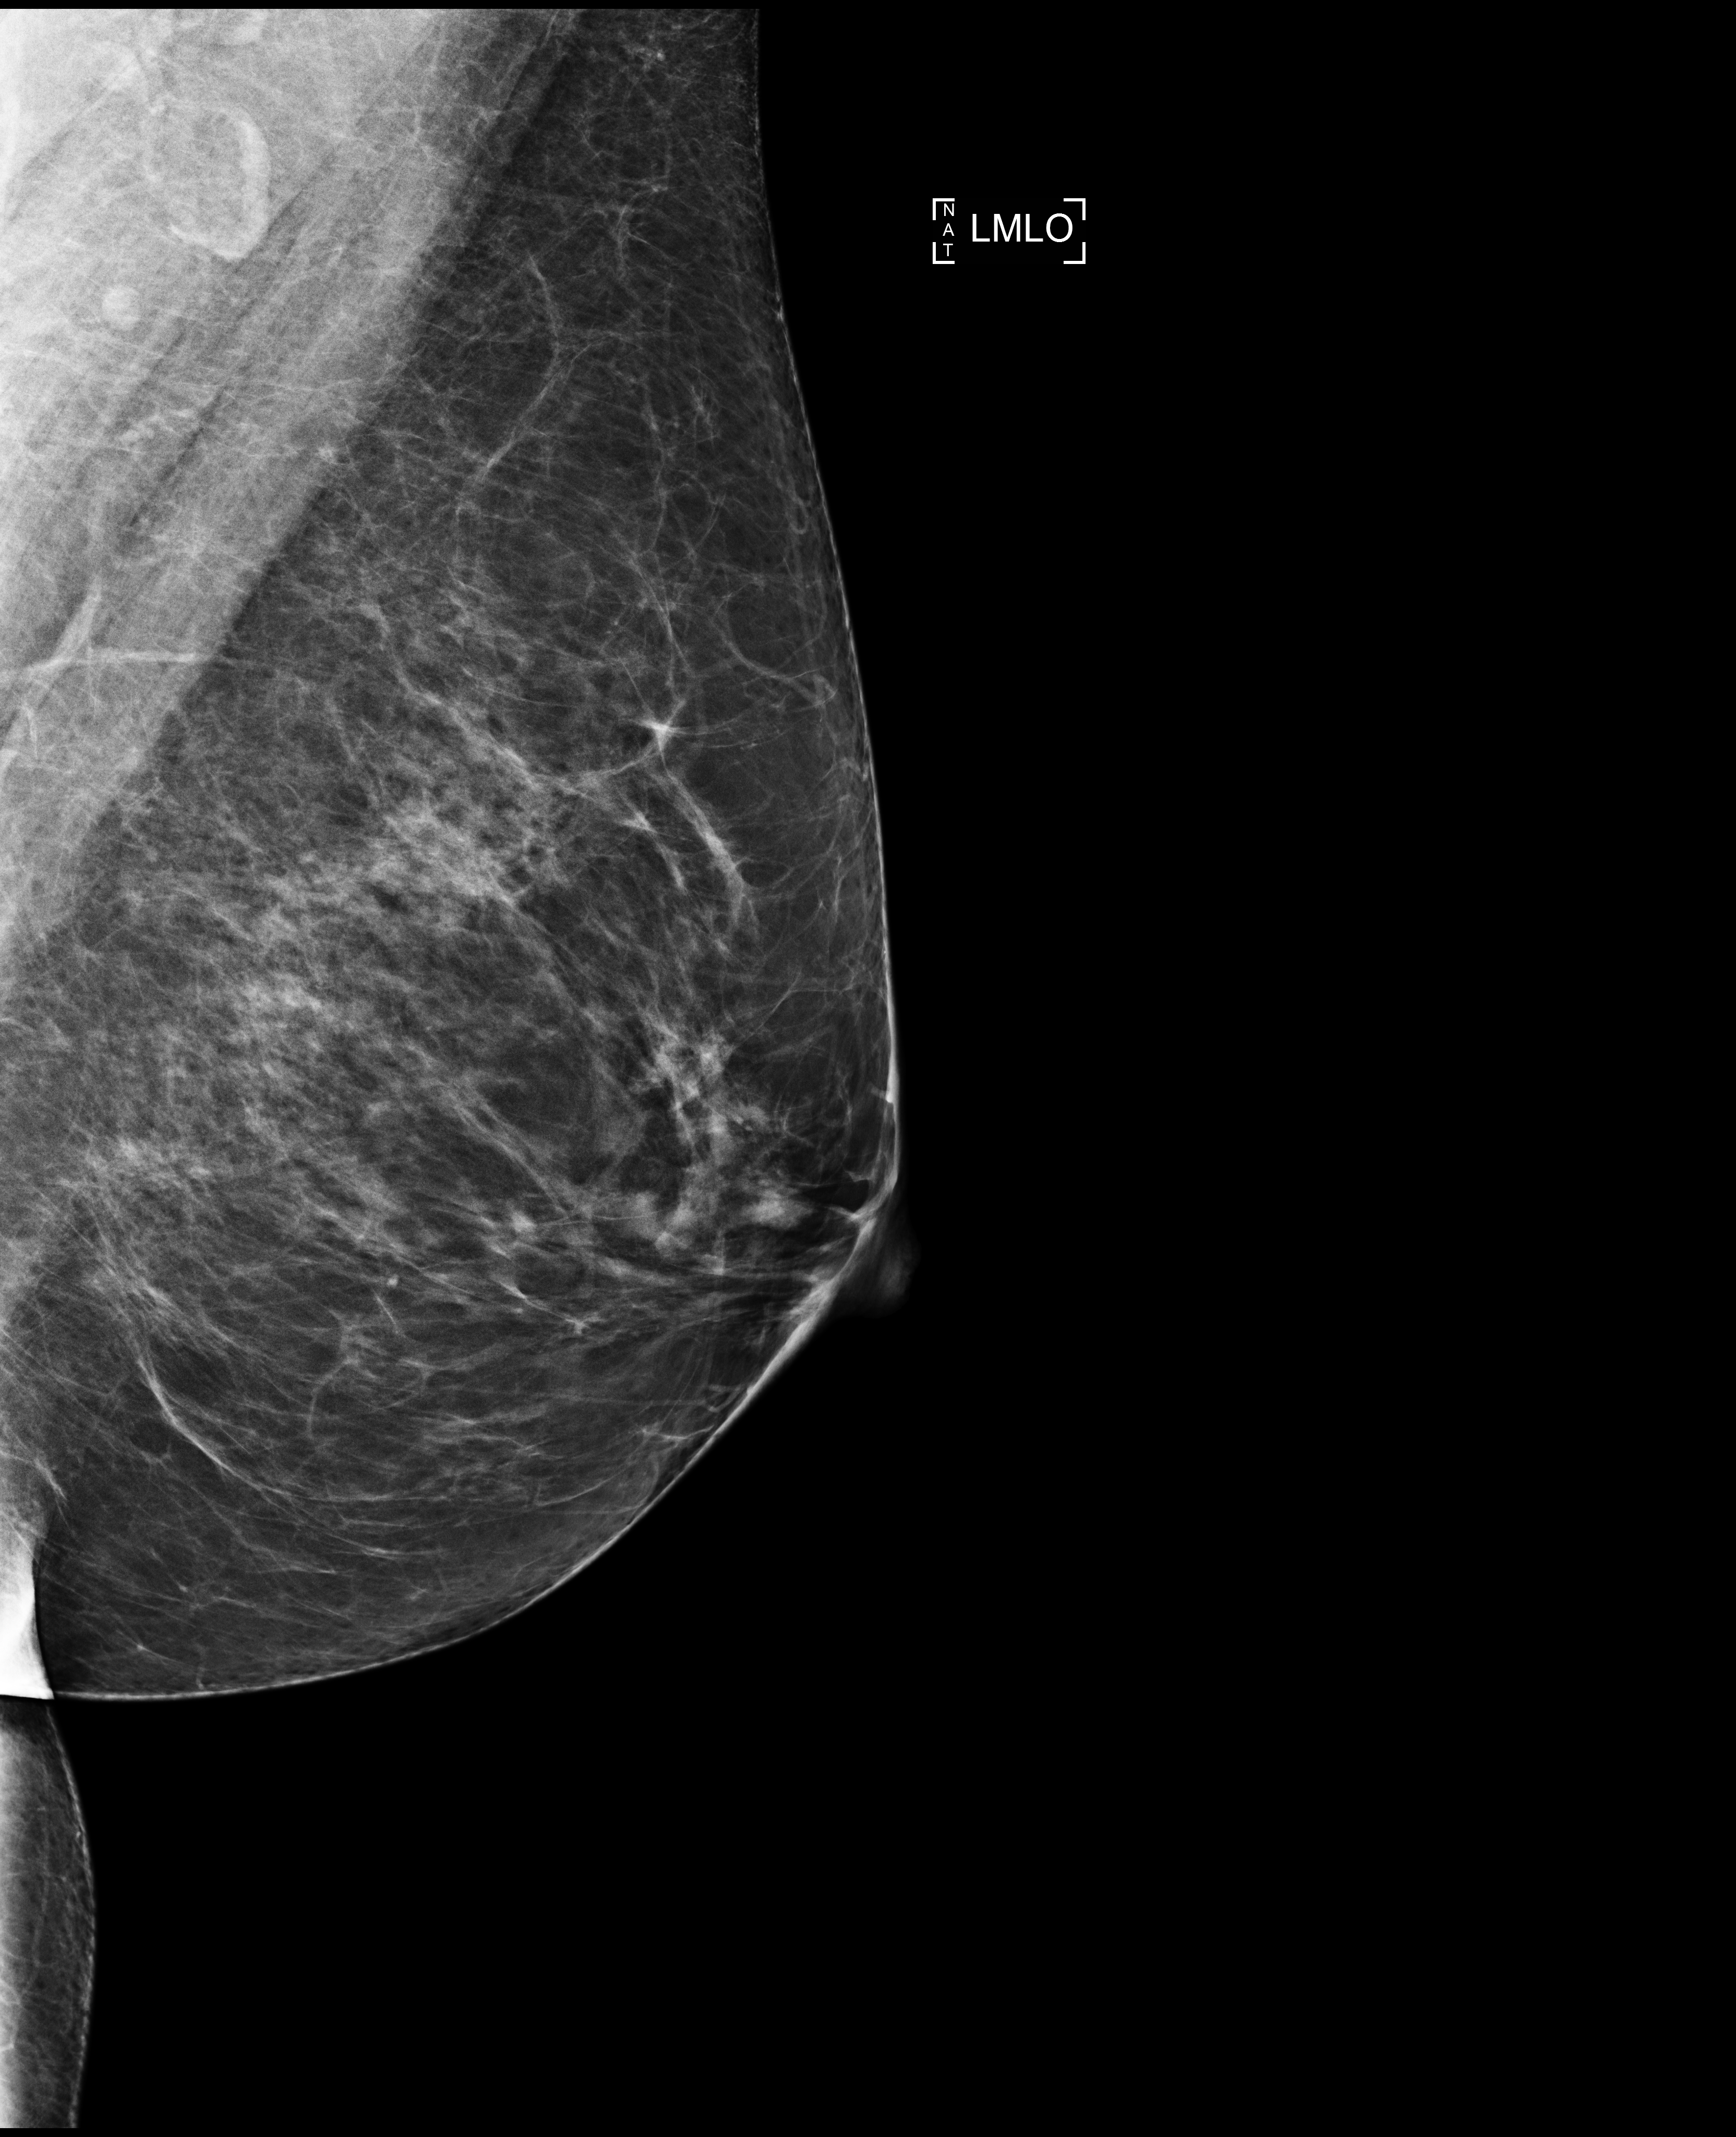
Full-field digital mammogram (FFDM), left breast, medio-lateral oblique projection, annual screening mammography examination, compressed breast thickness 92 mm, system: Selenia Dimensions. Patient: female, 52 years.
BI-RADS breast density category at the screening exam (both breasts, scale 1–4): 2. Final BI-RADS assessment for this screening round (tomosynthesis exam, both breasts): category 1. Recall: no recall after this screen.